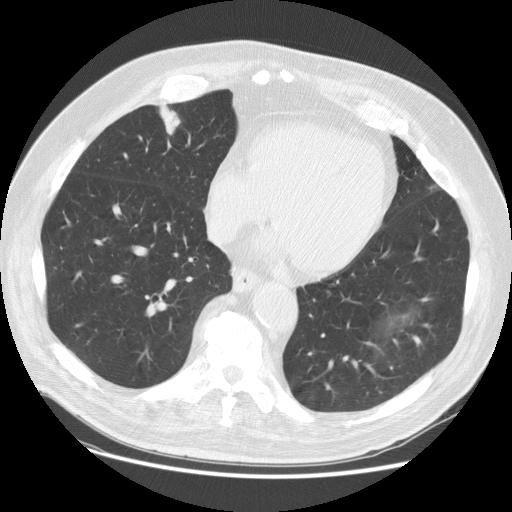
Axial slice from a low-dose chest CT screening exam. First (baseline) screen. Lung window (W 1500 / L -600 HU). 140 kVp. Slice 89 of 129 in the series. 512 × 512 image matrix. Male, age 74 years at enrolment.
• Expert-annotated lung lesion, box from (x=148, y=94) to (x=186, y=144) px.
• Reader record for this screening exam (exam-level; its link to the box is not recorded): non-calcified nodule or mass ≥4 mm, right middle lobe, 24 × 24 mm, spiculated (stellate) margins, soft tissue attenuation.
• Official screen result: positive, change unspecified: nodule(s) >= 4 mm or enlarging nodule(s), mass(es), or other non-specific abnormalities suspicious for lung cancer.
• Participant outcome: lung cancer diagnosed 296 days after this screen — papillary adenocarcinoma, NOS, right middle lobe, well differentiated (G1), stage IA (AJCC 6th edition), 20 mm at pathology.